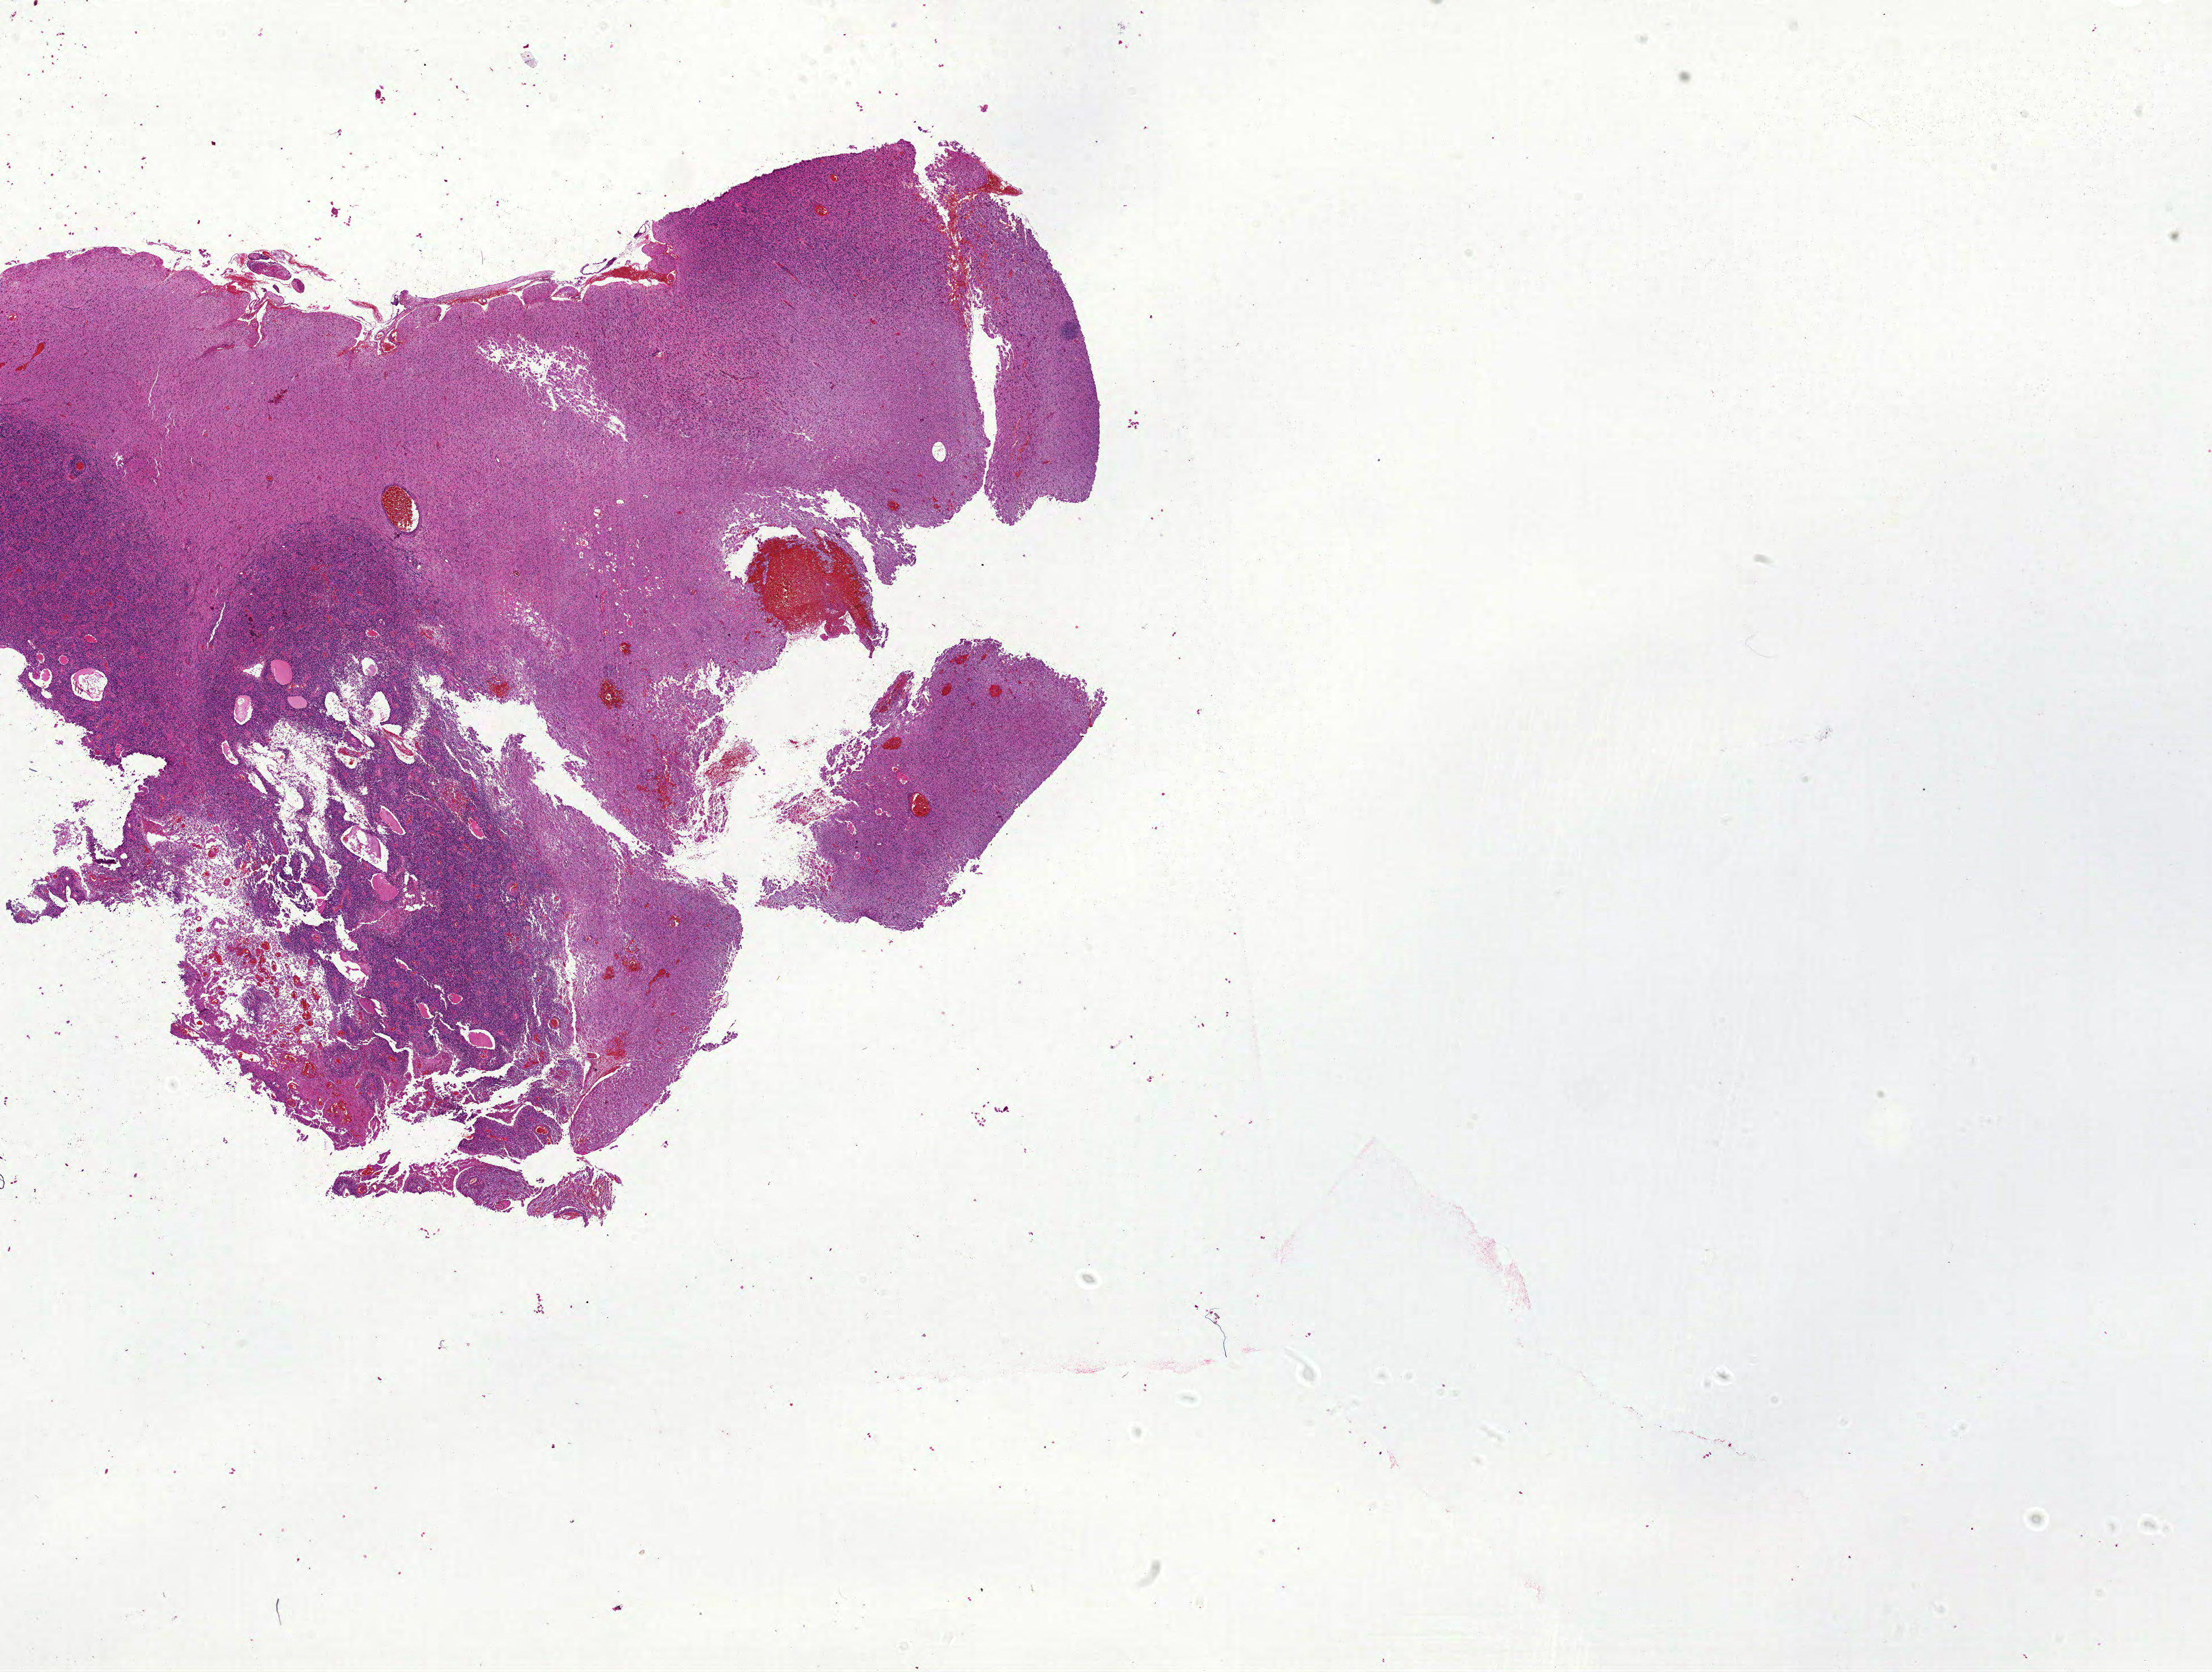
Whole-slide histology image, H&E-stained — a low-resolution overview of the entire scanned area, about 31.0 x 23.4 mm (from a 20x scan); formalin-fixed paraffin-embedded (FFPE) diagnostic section; primary tumour sample from the brain. Male patient; age at initial diagnosis 62 years.
Pathologic diagnosis: Glioblastoma.